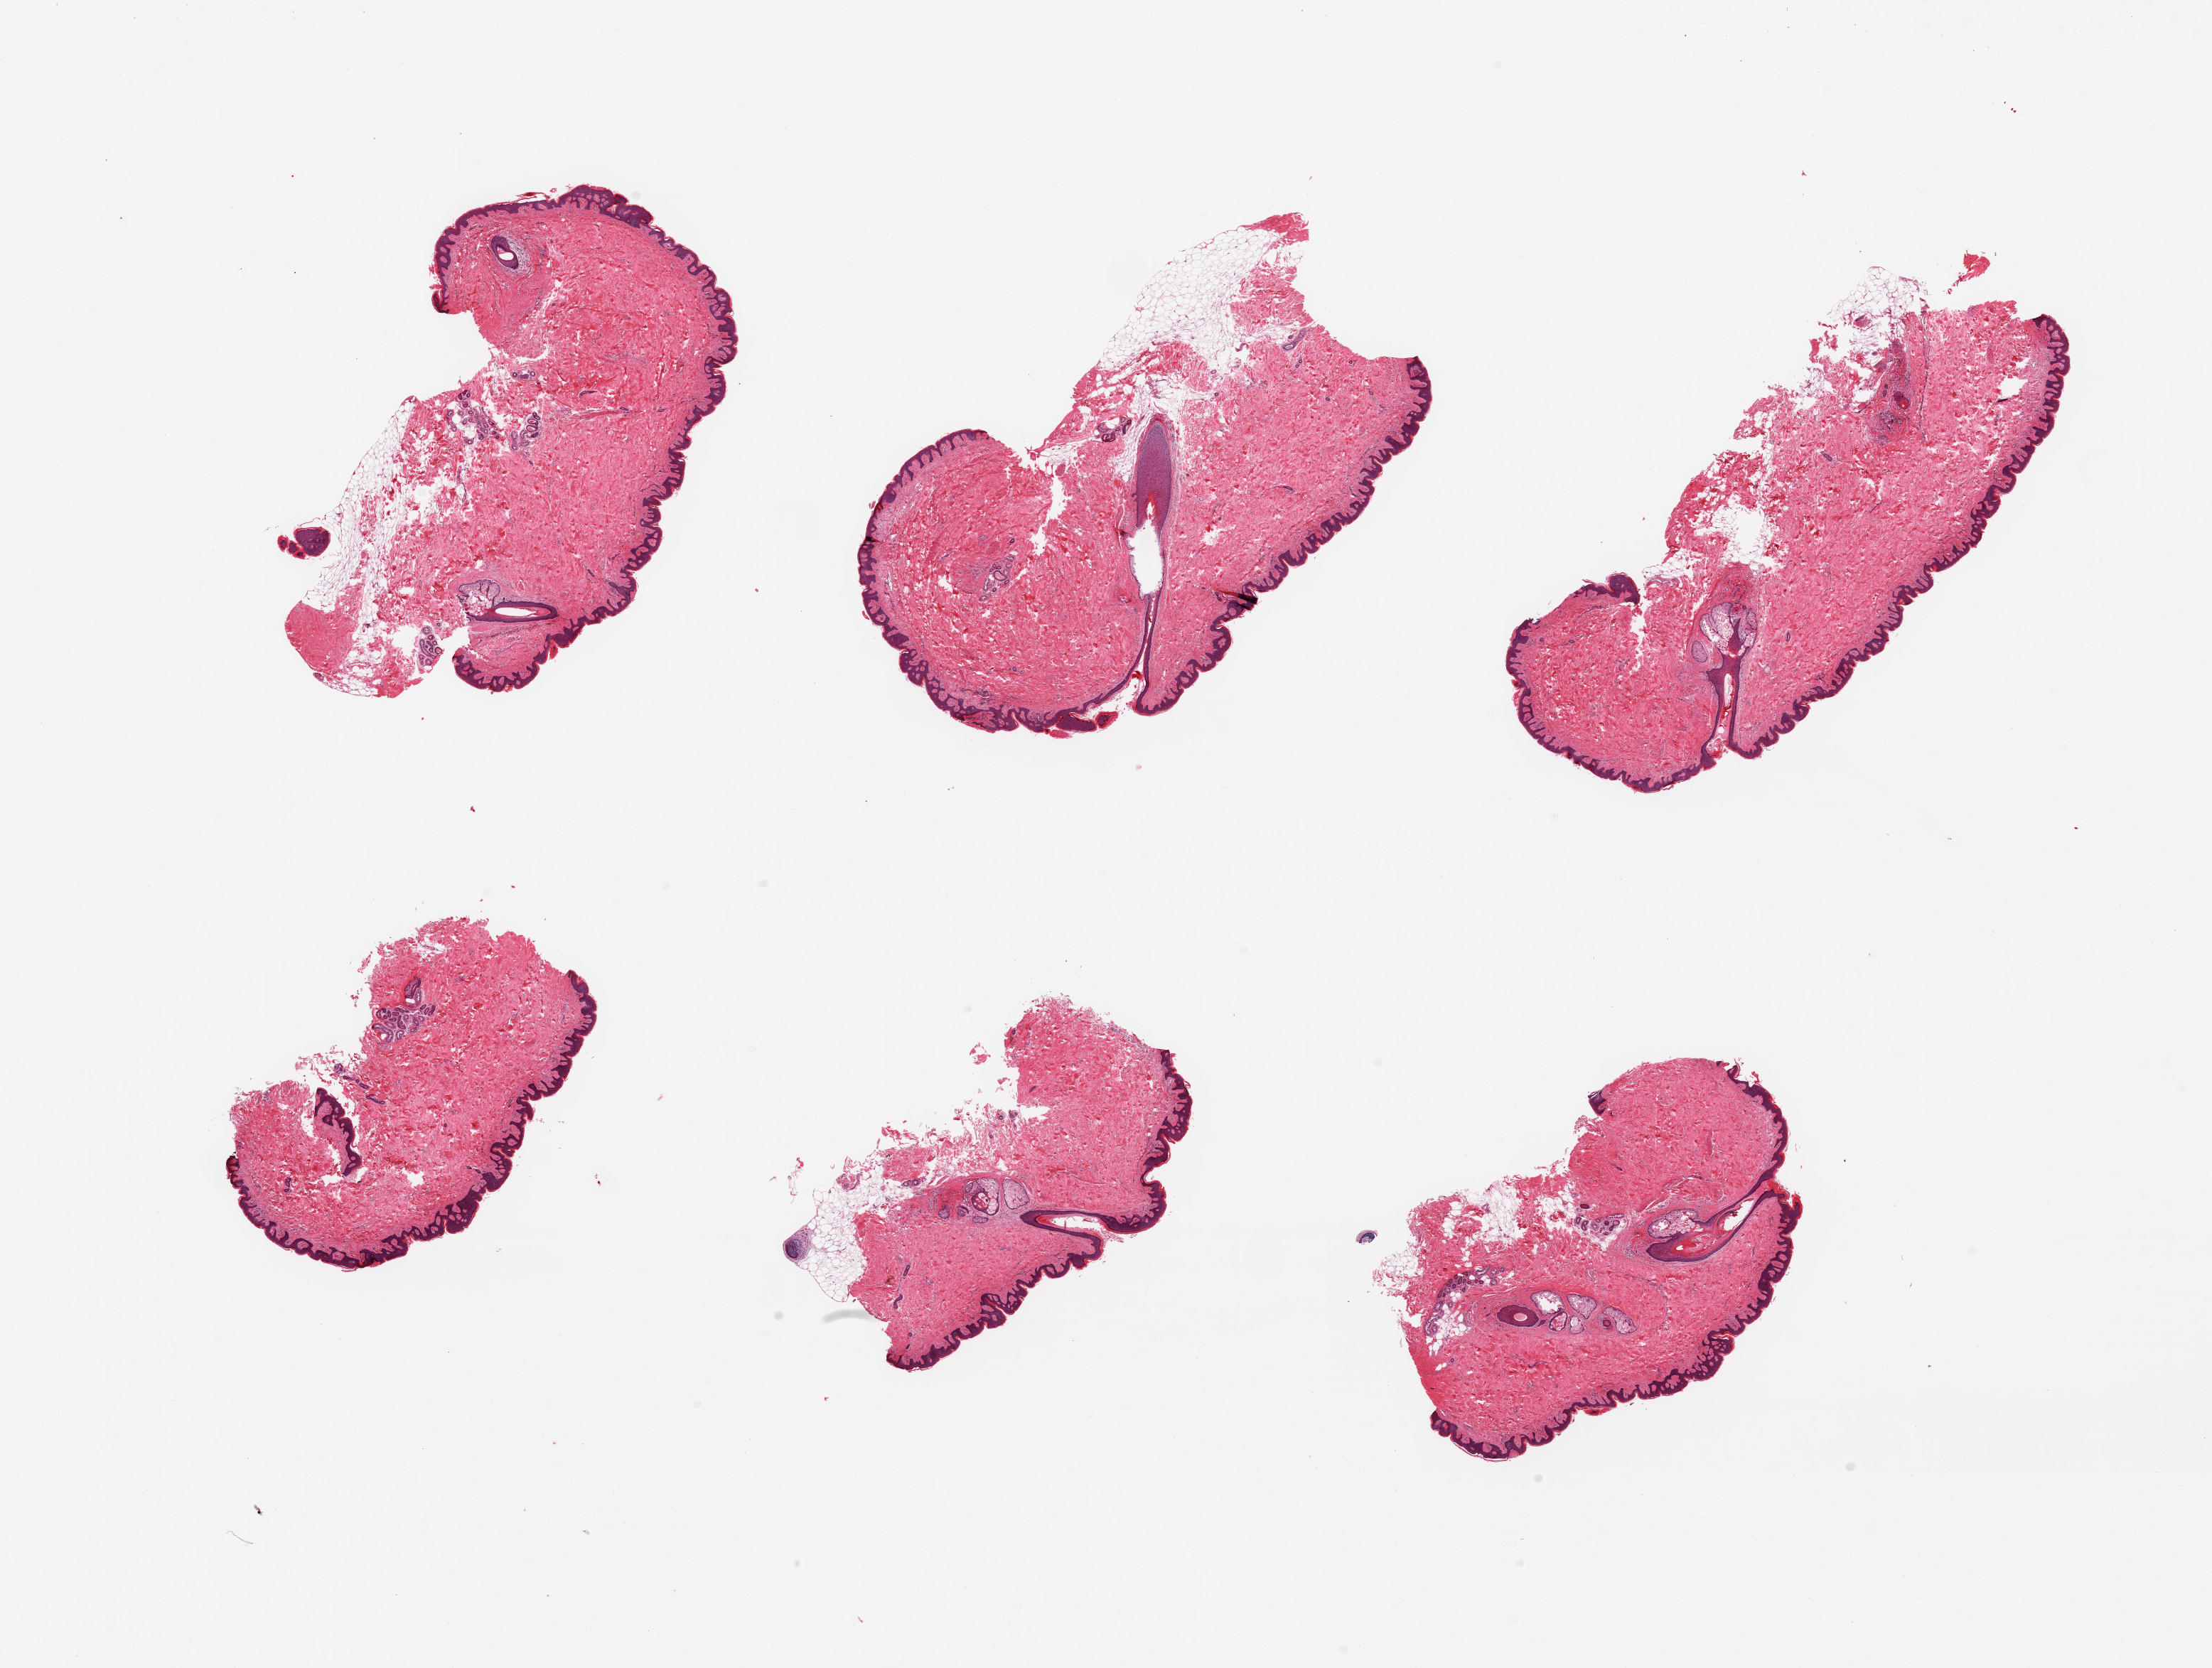
Digitized H&E-stained section, brightfield, shown as a low-resolution overview of the whole scanned area (about 24.6 x 18.6 mm). PAXgene-fixed paraffin-embedded (PFPE) section. Section of skin of suprapubic region (target tissue). Tissue donor sample.
Reviewer comment on this tissue sample: 6 pieces; well trimmed; up to 10% dermal fat.